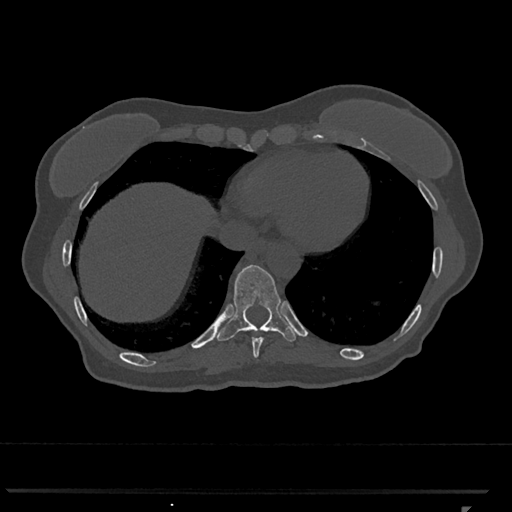
CT including the spine, one axial slice; slice 583 of 793 in the series (ordered by position); reconstruction kernel Br40s/3; 120 kVp; bone window (W 1800 / L 400 HU); 0.5 mm slice thickness; 512 × 512 image matrix. Female patient, age 62 years. From the clinical record (not read from this slice): primary cancer: renal.
Structures marked on this image (semi-automatically segmented with operator editing):
- T10 vertebra: bounding box <217,265,297,342> (left, top, right, bottom; pixels)
- T9 vertebra: <252,331,275,358>